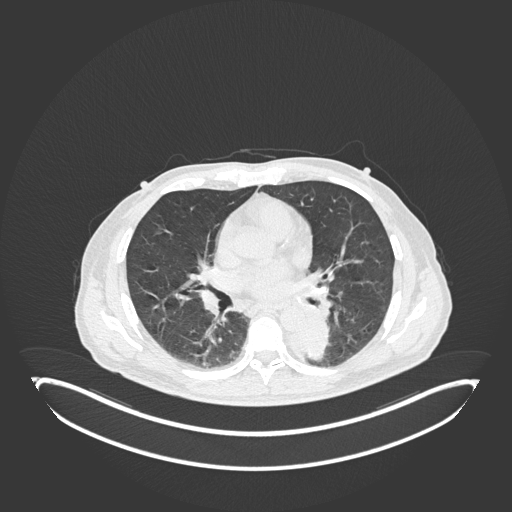
Chest CT, one axial slice; position 100 of 251 along the scan axis; reconstruction kernel B30f; 120 kVp; lung window (W 1500 / L -600 HU); 1 mm slice thickness; 512 × 512 image matrix, field of view 500 × 500 mm. Male patient, age 72 years. From the clinical record (not read from this slice): clinical TNM (as recorded): T2b N0 M1.
Annotated regions visible in this slice (bounding box drawn by a radiologist):
- lung tumour (recorded histology: adenocarcinoma): bounding box (x1, y1, x2, y2) in pixels: (286, 317, 332, 364)